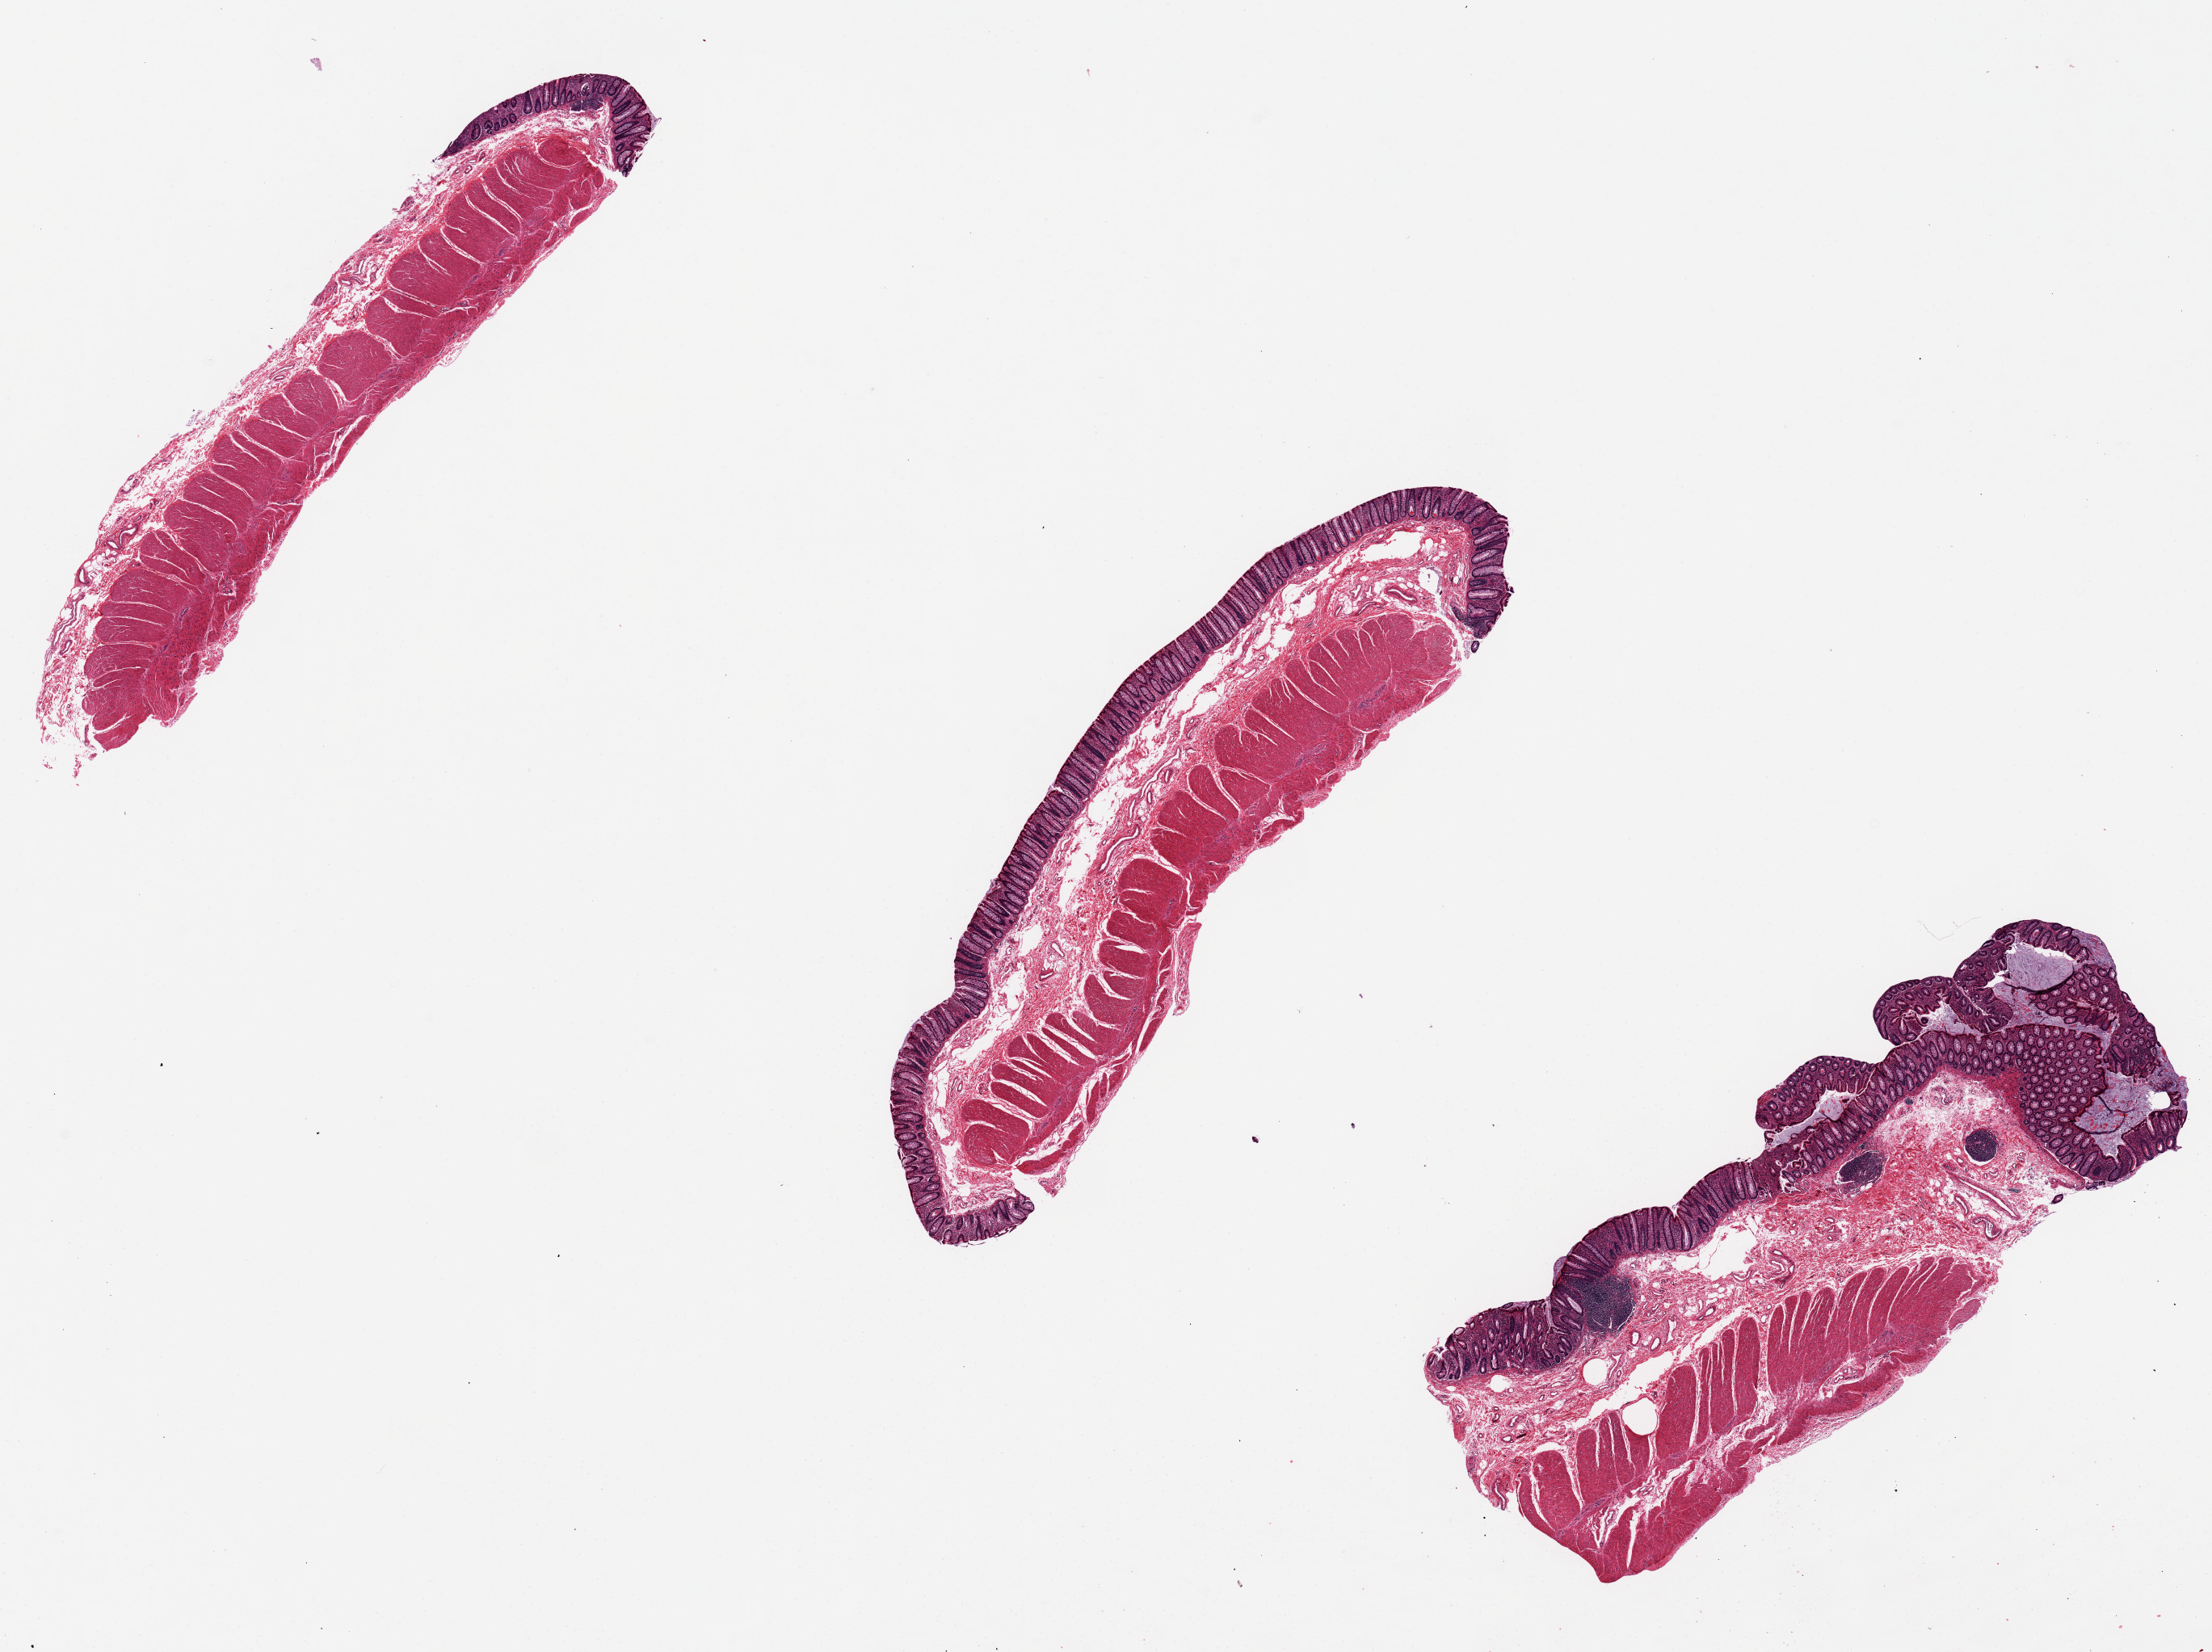
Digitized hematoxylin and eosin (H&E)-stained section, brightfield — shown as a low-resolution overview of the whole scanned area (about 21.7 x 16.2 mm), PAXgene-fixed paraffin-embedded (PFPE) section, sampled site (target tissue): transverse colon, tissue donor sample. Female donor.
* review note (as recorded): Well preserved. Abundant mucosa in 2 pieces; sparse mucosa in 1